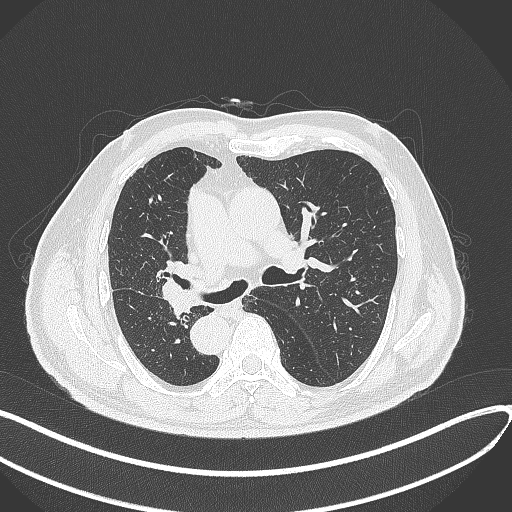
Chest CT, one axial slice; slice 175 of 300 in the series (ordered by position); reconstruction kernel B70f; lung window (W 1500 / L -600 HU); 1 mm slice thickness; 512 × 512 image matrix. Patient: male, 67 years. Case-level facts recorded for this patient, not image findings: clinical TNM (as recorded): T2a N0 M0.
Outlined on this slice (bounding box drawn by a radiologist):
- lung tumour (recorded histology: squamous cell carcinoma): bounding box (x1, y1, x2, y2) in pixels: (158, 273, 201, 319)